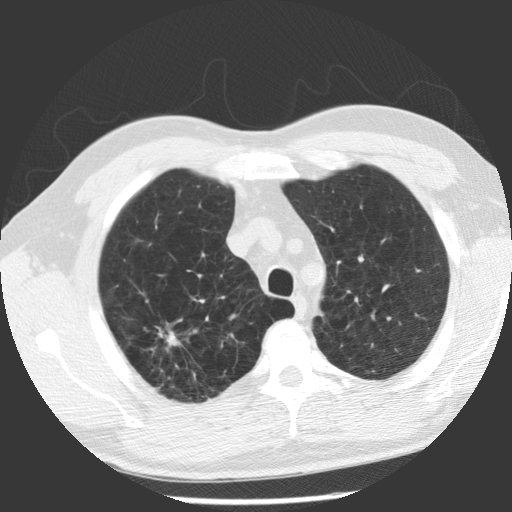
Chest CT (low-dose screening protocol), one axial image; baseline screening round; lung window (W 1500 / L -600 HU); 140 kVp. Male, age 62 years at enrolment. Former smoker at enrolment.
Expert-annotated lung lesion, bounding box [x1, y1, x2, y2] px = [121, 302, 202, 384]. The screening reader recorded 2 non-calcified nodules or masses ≥4 mm on this exam (right upper lobe, right upper lobe); which of them this box marks is not recorded. Later outcome: lung cancer diagnosed 71 days after this screen — adenocarcinoma, NOS, right upper lobe, poorly differentiated (G3), stage IV (AJCC 6th edition), 30 mm at pathology.